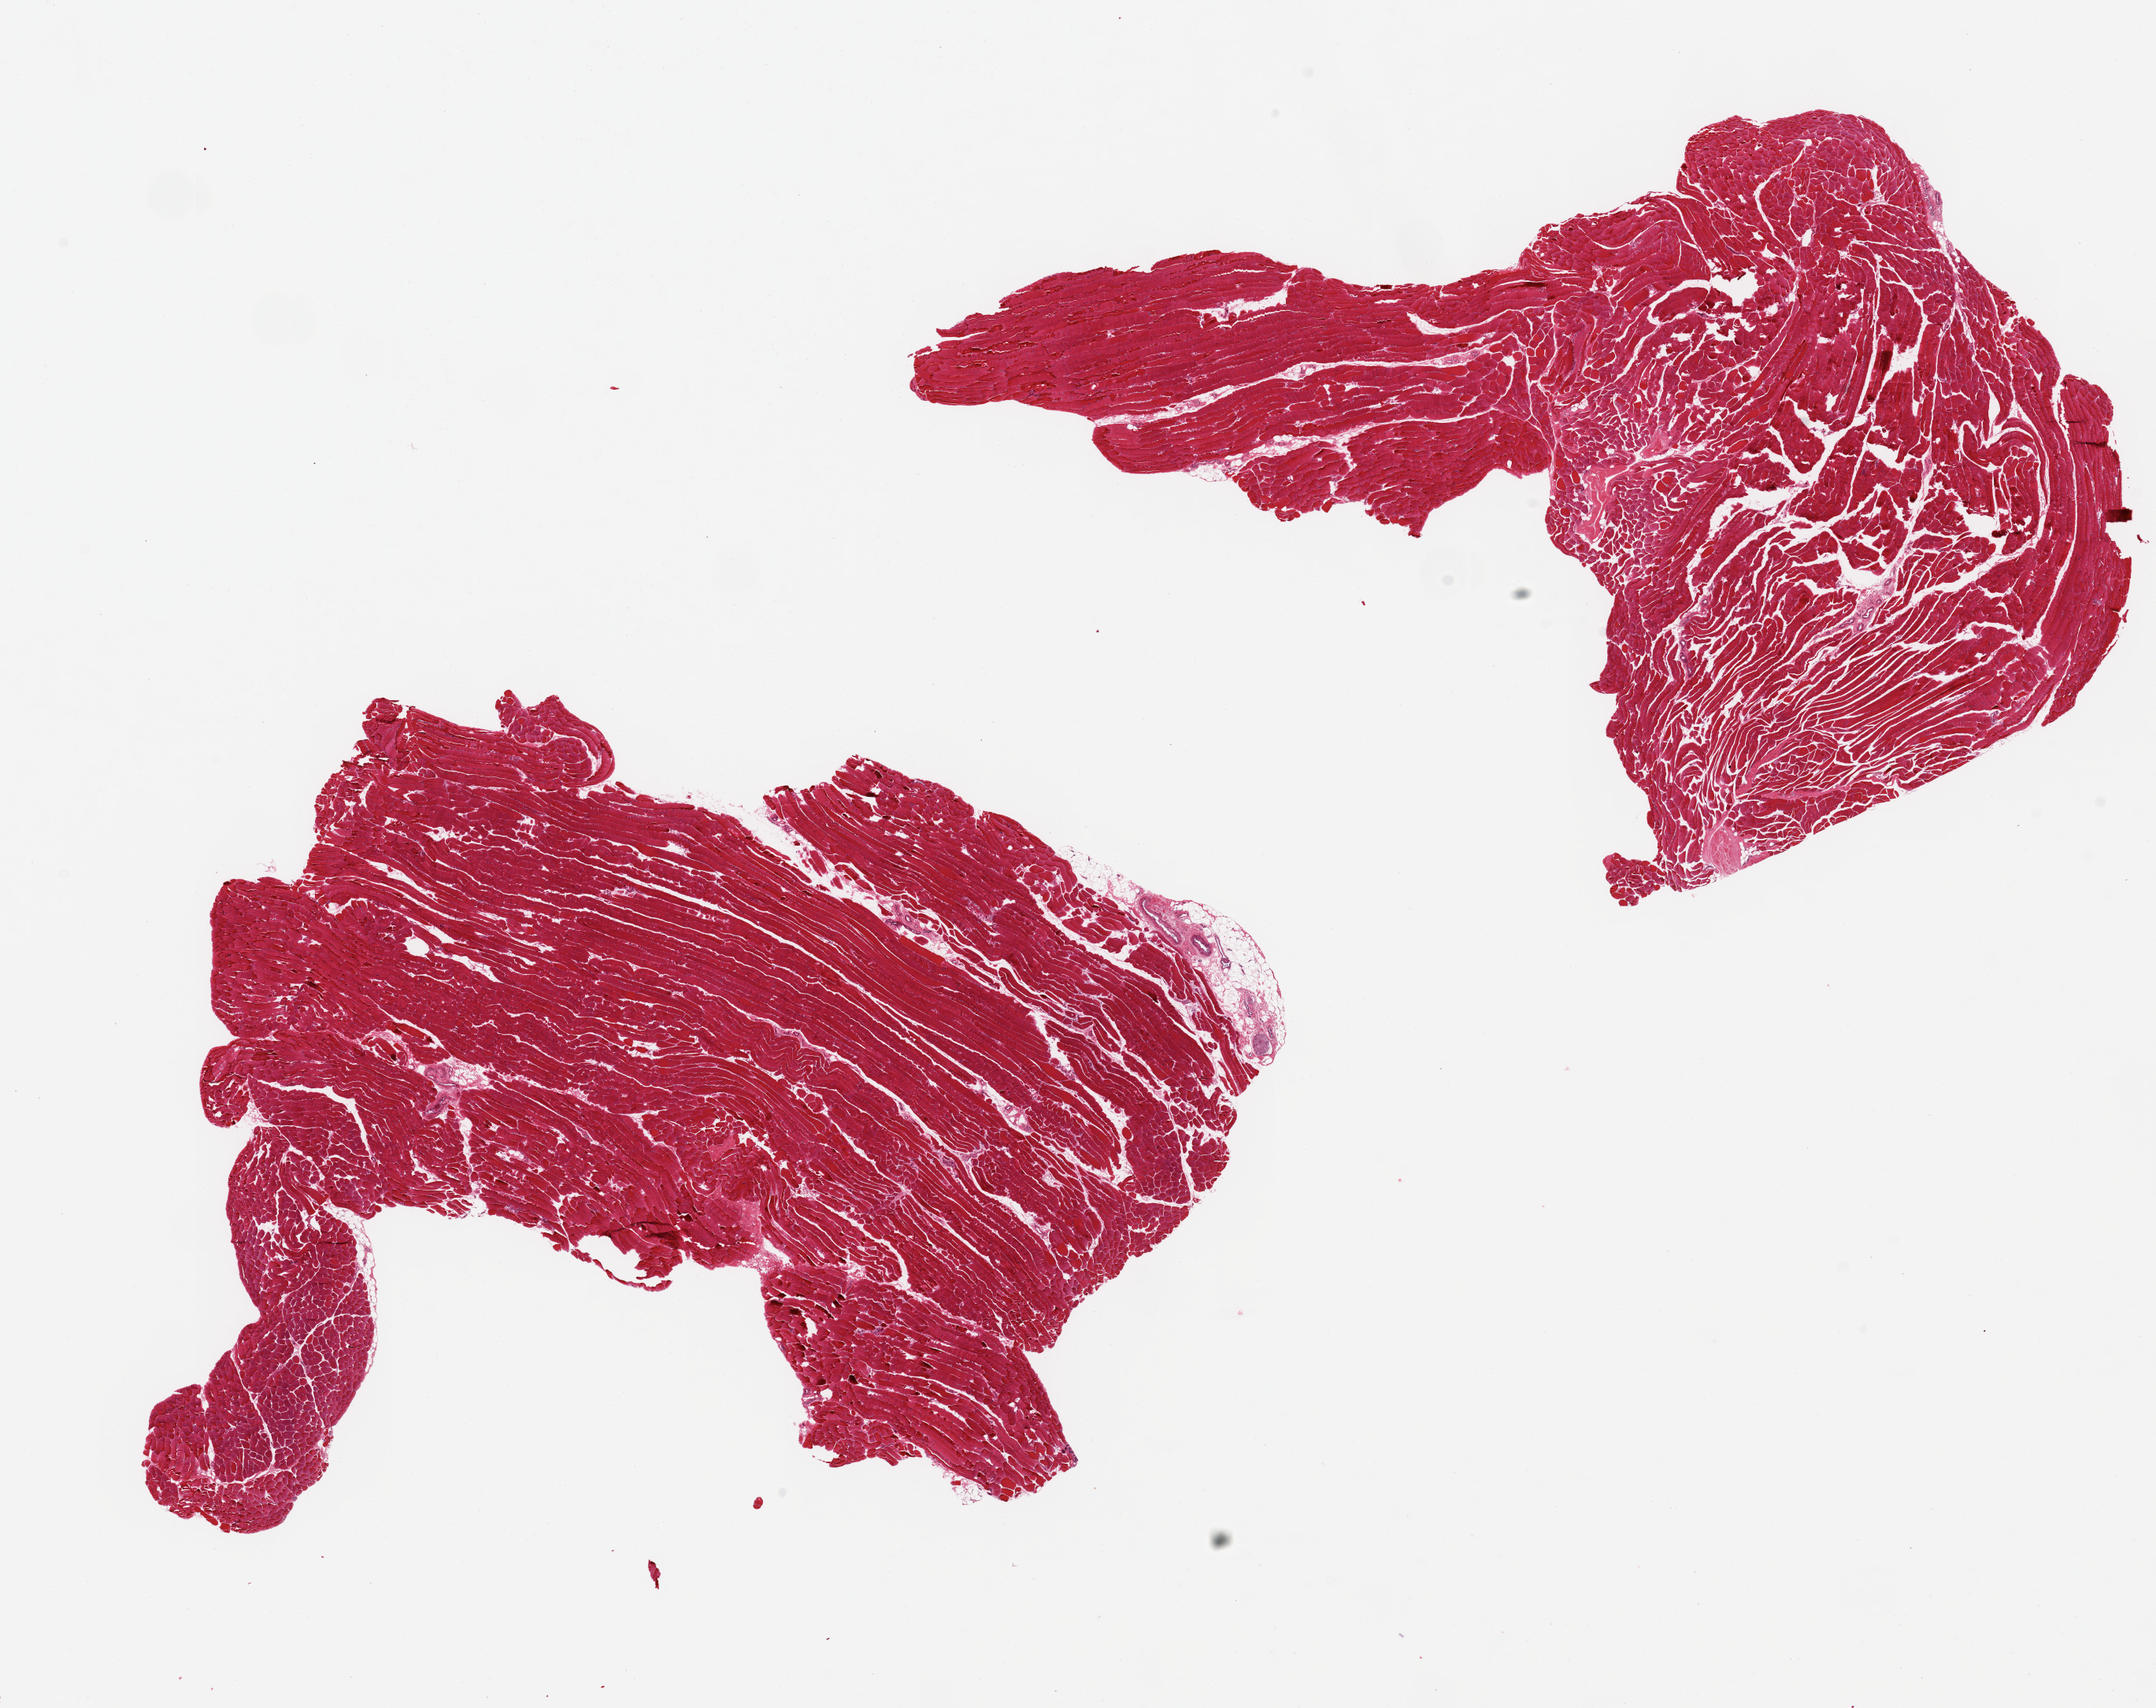
H&E whole-slide image — whole scanned area (about 21.7 x 17.2 mm) shown as a low-resolution overview, PAXgene-fixed, paraffin-embedded tissue, target tissue: skeletal muscle, tissue donor sample. Female donor.
Review note (as recorded): 2 pieces, 10x6.5 & 10x6mm; <5% extraneous adipose.